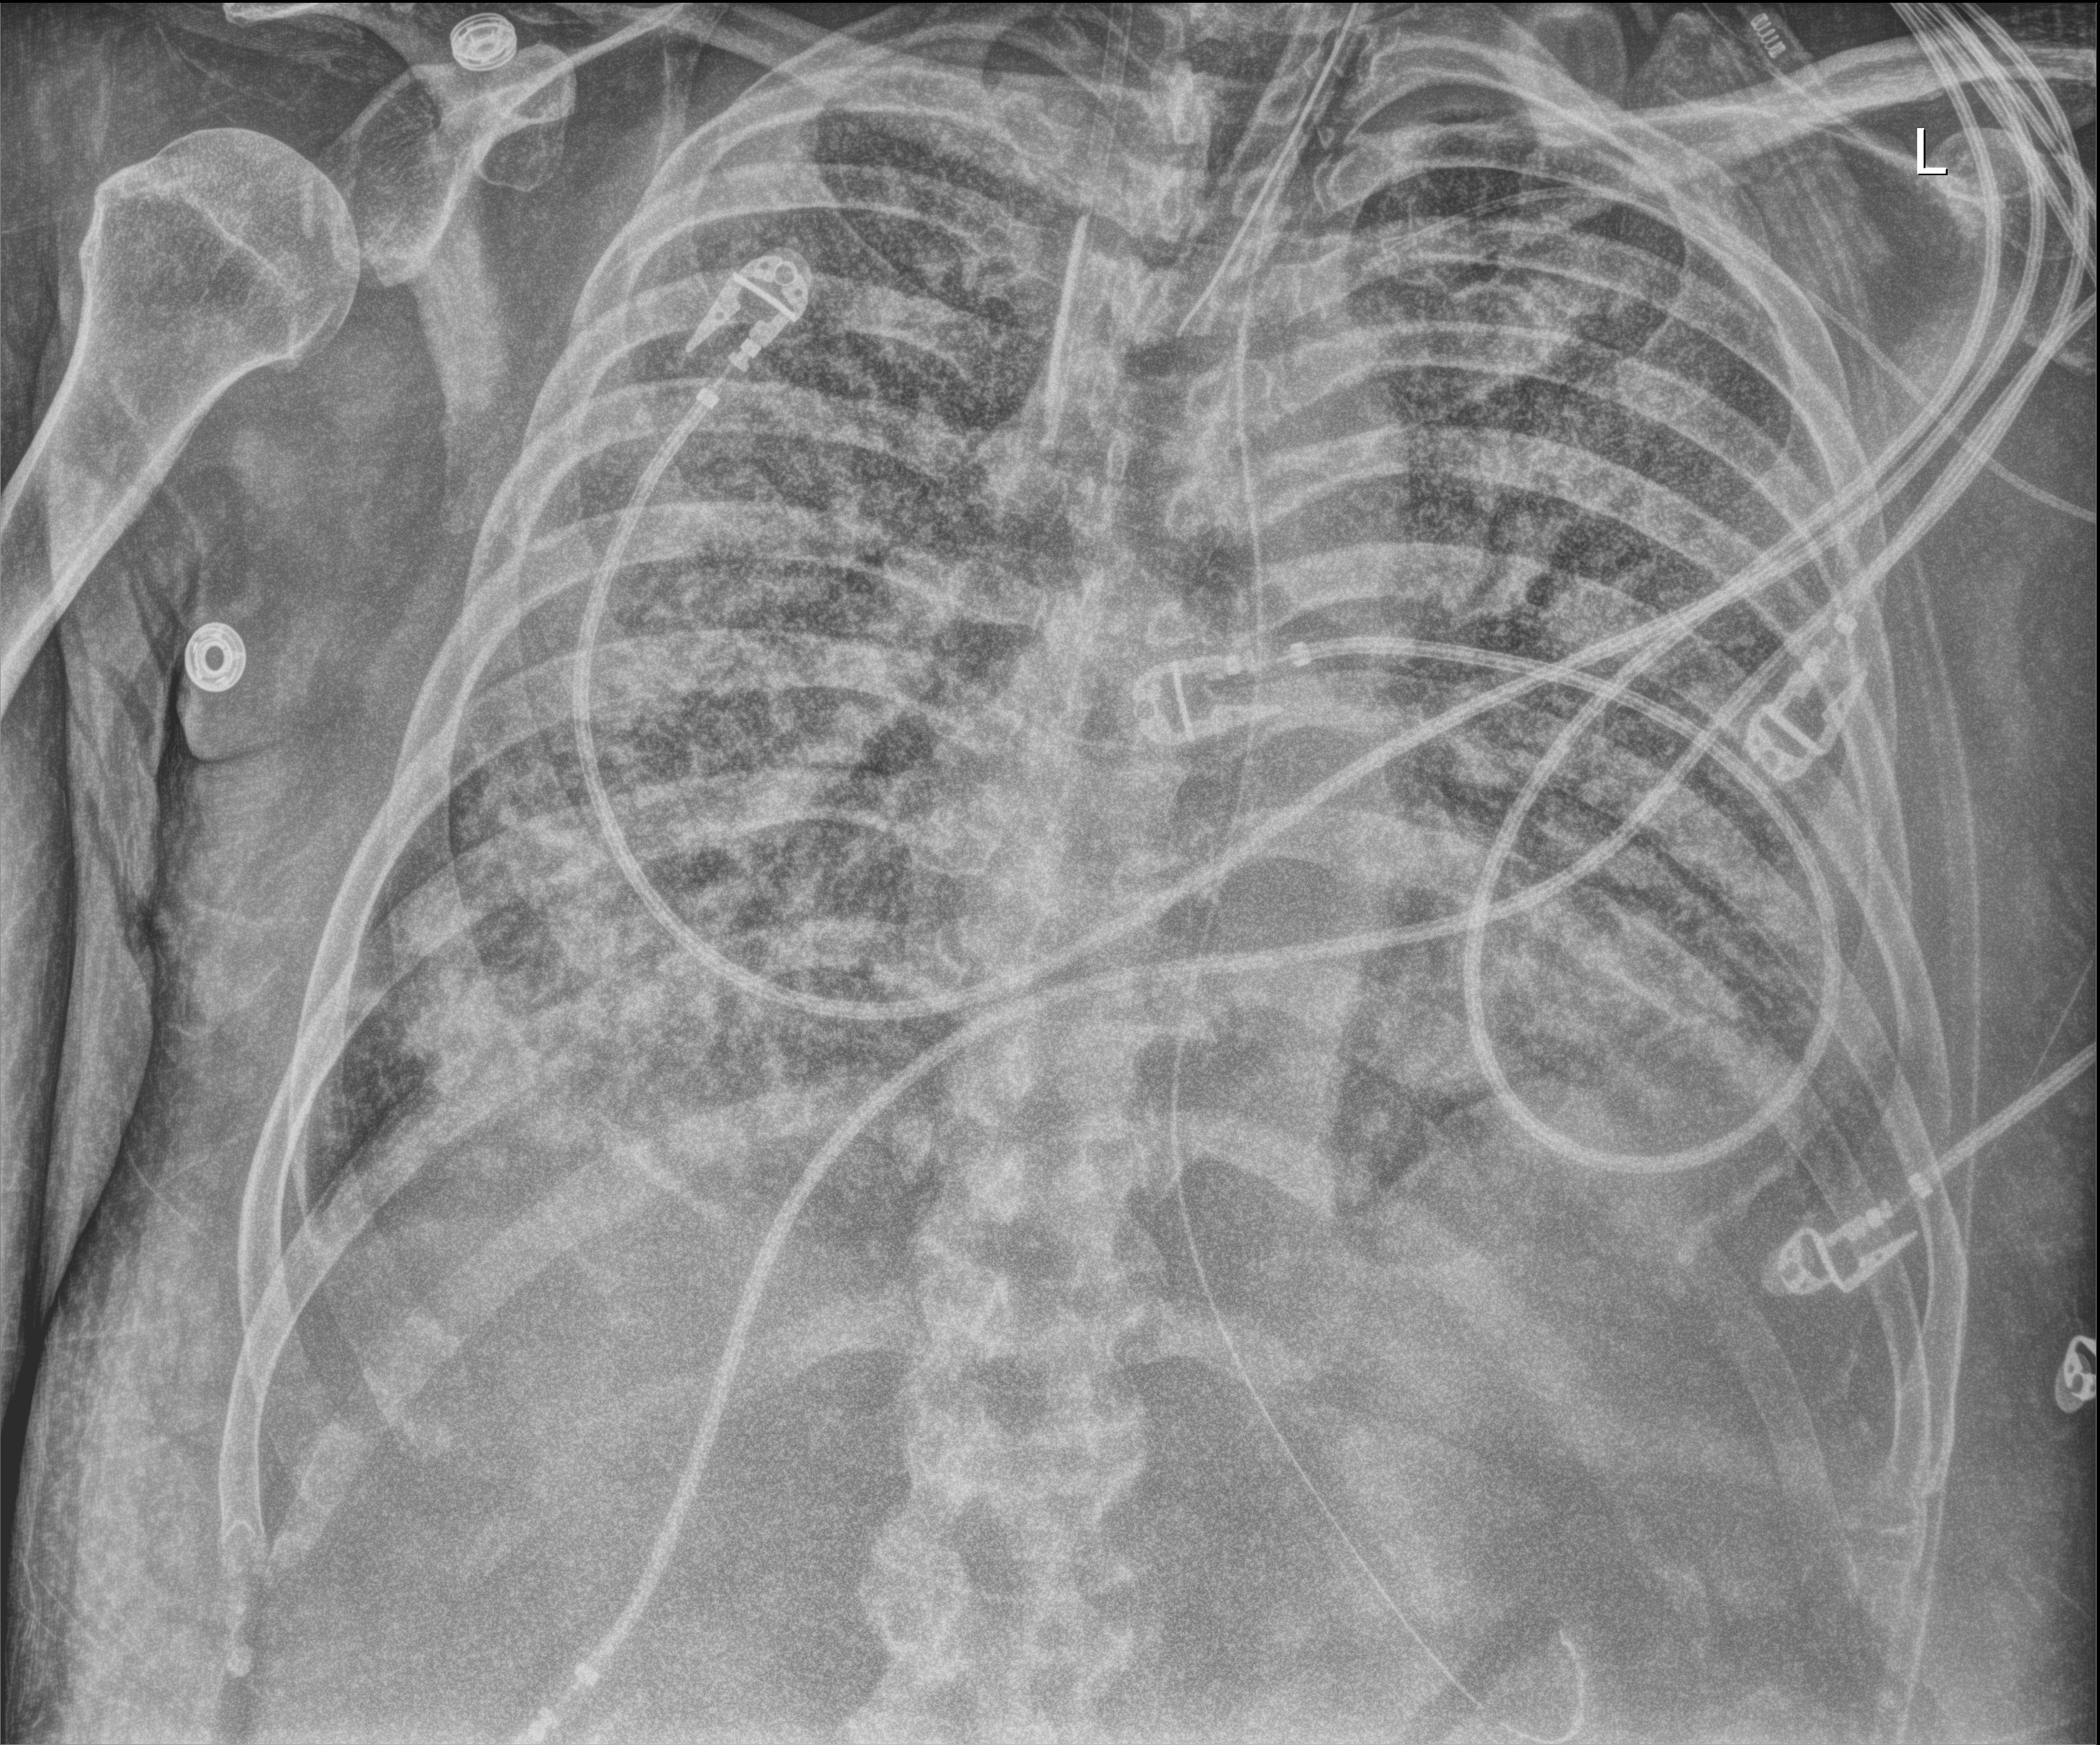
Bedside chest radiograph (digital radiography), anteroposterior (AP) projection. Patient hospitalised with COVID-19; male, aged 60–74 years.
From the hospital-stay record, not from the radiograph (when in the stay this image was taken is not recorded): mechanically ventilated during this hospital stay: yes.